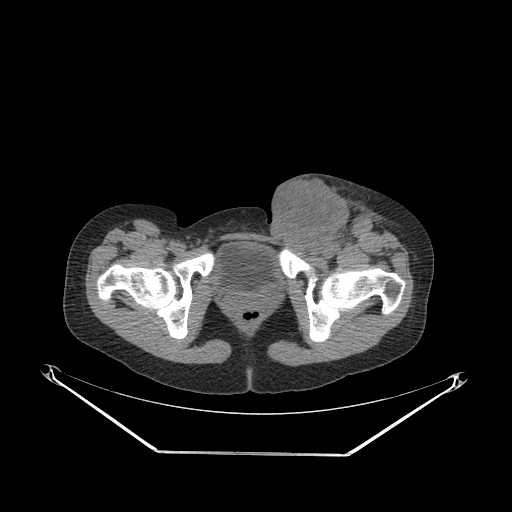
CT of an extremity soft-tissue mass (from a PET/CT study), one axial slice; position 66 of 267 along the scan axis; reconstruction kernel SOFT; soft-tissue window (W 400 / L 40 HU); 3.75 mm slice thickness; 512 × 512 image matrix. Female patient. From the clinical record (not read from this slice): histological type: leiomyosarcoma; grade: high; site of the primary tumour: groin.
Annotated regions visible in this slice (expert contour drawn on MRI and transferred to this co-registered scan by the dataset authors):
- gross tumour volume including surrounding oedema: bounding box [x1, y1, x2, y2] px = [263, 178, 385, 255]
- gross tumour volume (mass): [265, 180, 348, 254]